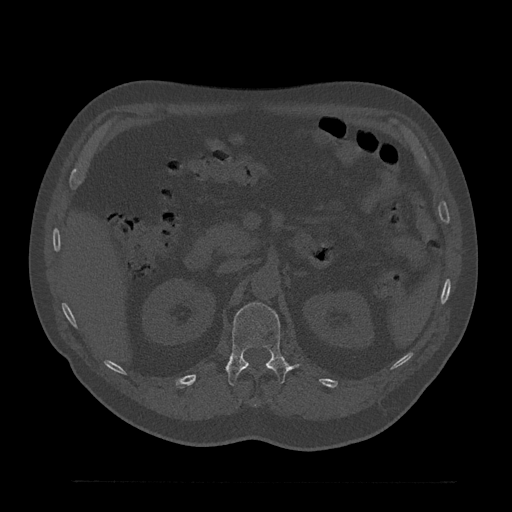
CT including the spine, one axial slice; slice 180 of 797 in the series (ordered by position); reconstruction kernel Br40s/3; 120 kVp; bone window (W 1800 / L 400 HU); 512 × 512 image matrix, field of view 430 × 430 mm. Male patient, age 61 years. Case-level facts recorded for this patient, not image findings: primary cancer: prostate.
Annotated regions visible in this slice (semi-automatically segmented with operator editing):
- L1 vertebra: bounding box [x1, y1, x2, y2] px = [226, 303, 292, 386]
- T12 vertebra: [255, 403, 259, 407]